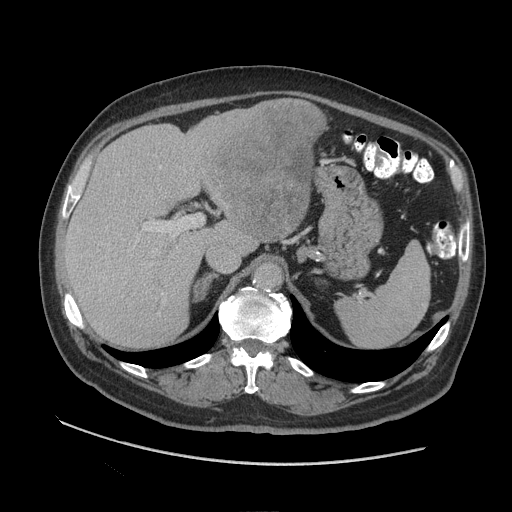
Contrast-enhanced abdominal CT (liver protocol), one axial slice; position 61 of 109 along the scan axis; reconstruction kernel STANDARD; 140 kVp; soft-tissue window (W 400 / L 40 HU); 512 × 512 image matrix, field of view 420 × 420 mm. Case-level facts recorded for this patient, not image findings: diagnosis: hepatocellular carcinoma (patient treated with transarterial chemoembolisation; whether this scan precedes or follows treatment is not stated here); TNM stage (as recorded): Stage-I; Child-Pugh class: A; tumour nodularity: uninodular.
Outlined on this slice (semi-automatically segmented with operator editing):
- liver parenchyma outside the tumour (the mass and vessels are separate outlines, so this box may not span the whole liver): box from (x=64, y=98) to (x=292, y=348) px
- mass: (x=194, y=98)–(x=327, y=241)
- liver vessels: (x=109, y=166)–(x=181, y=300)